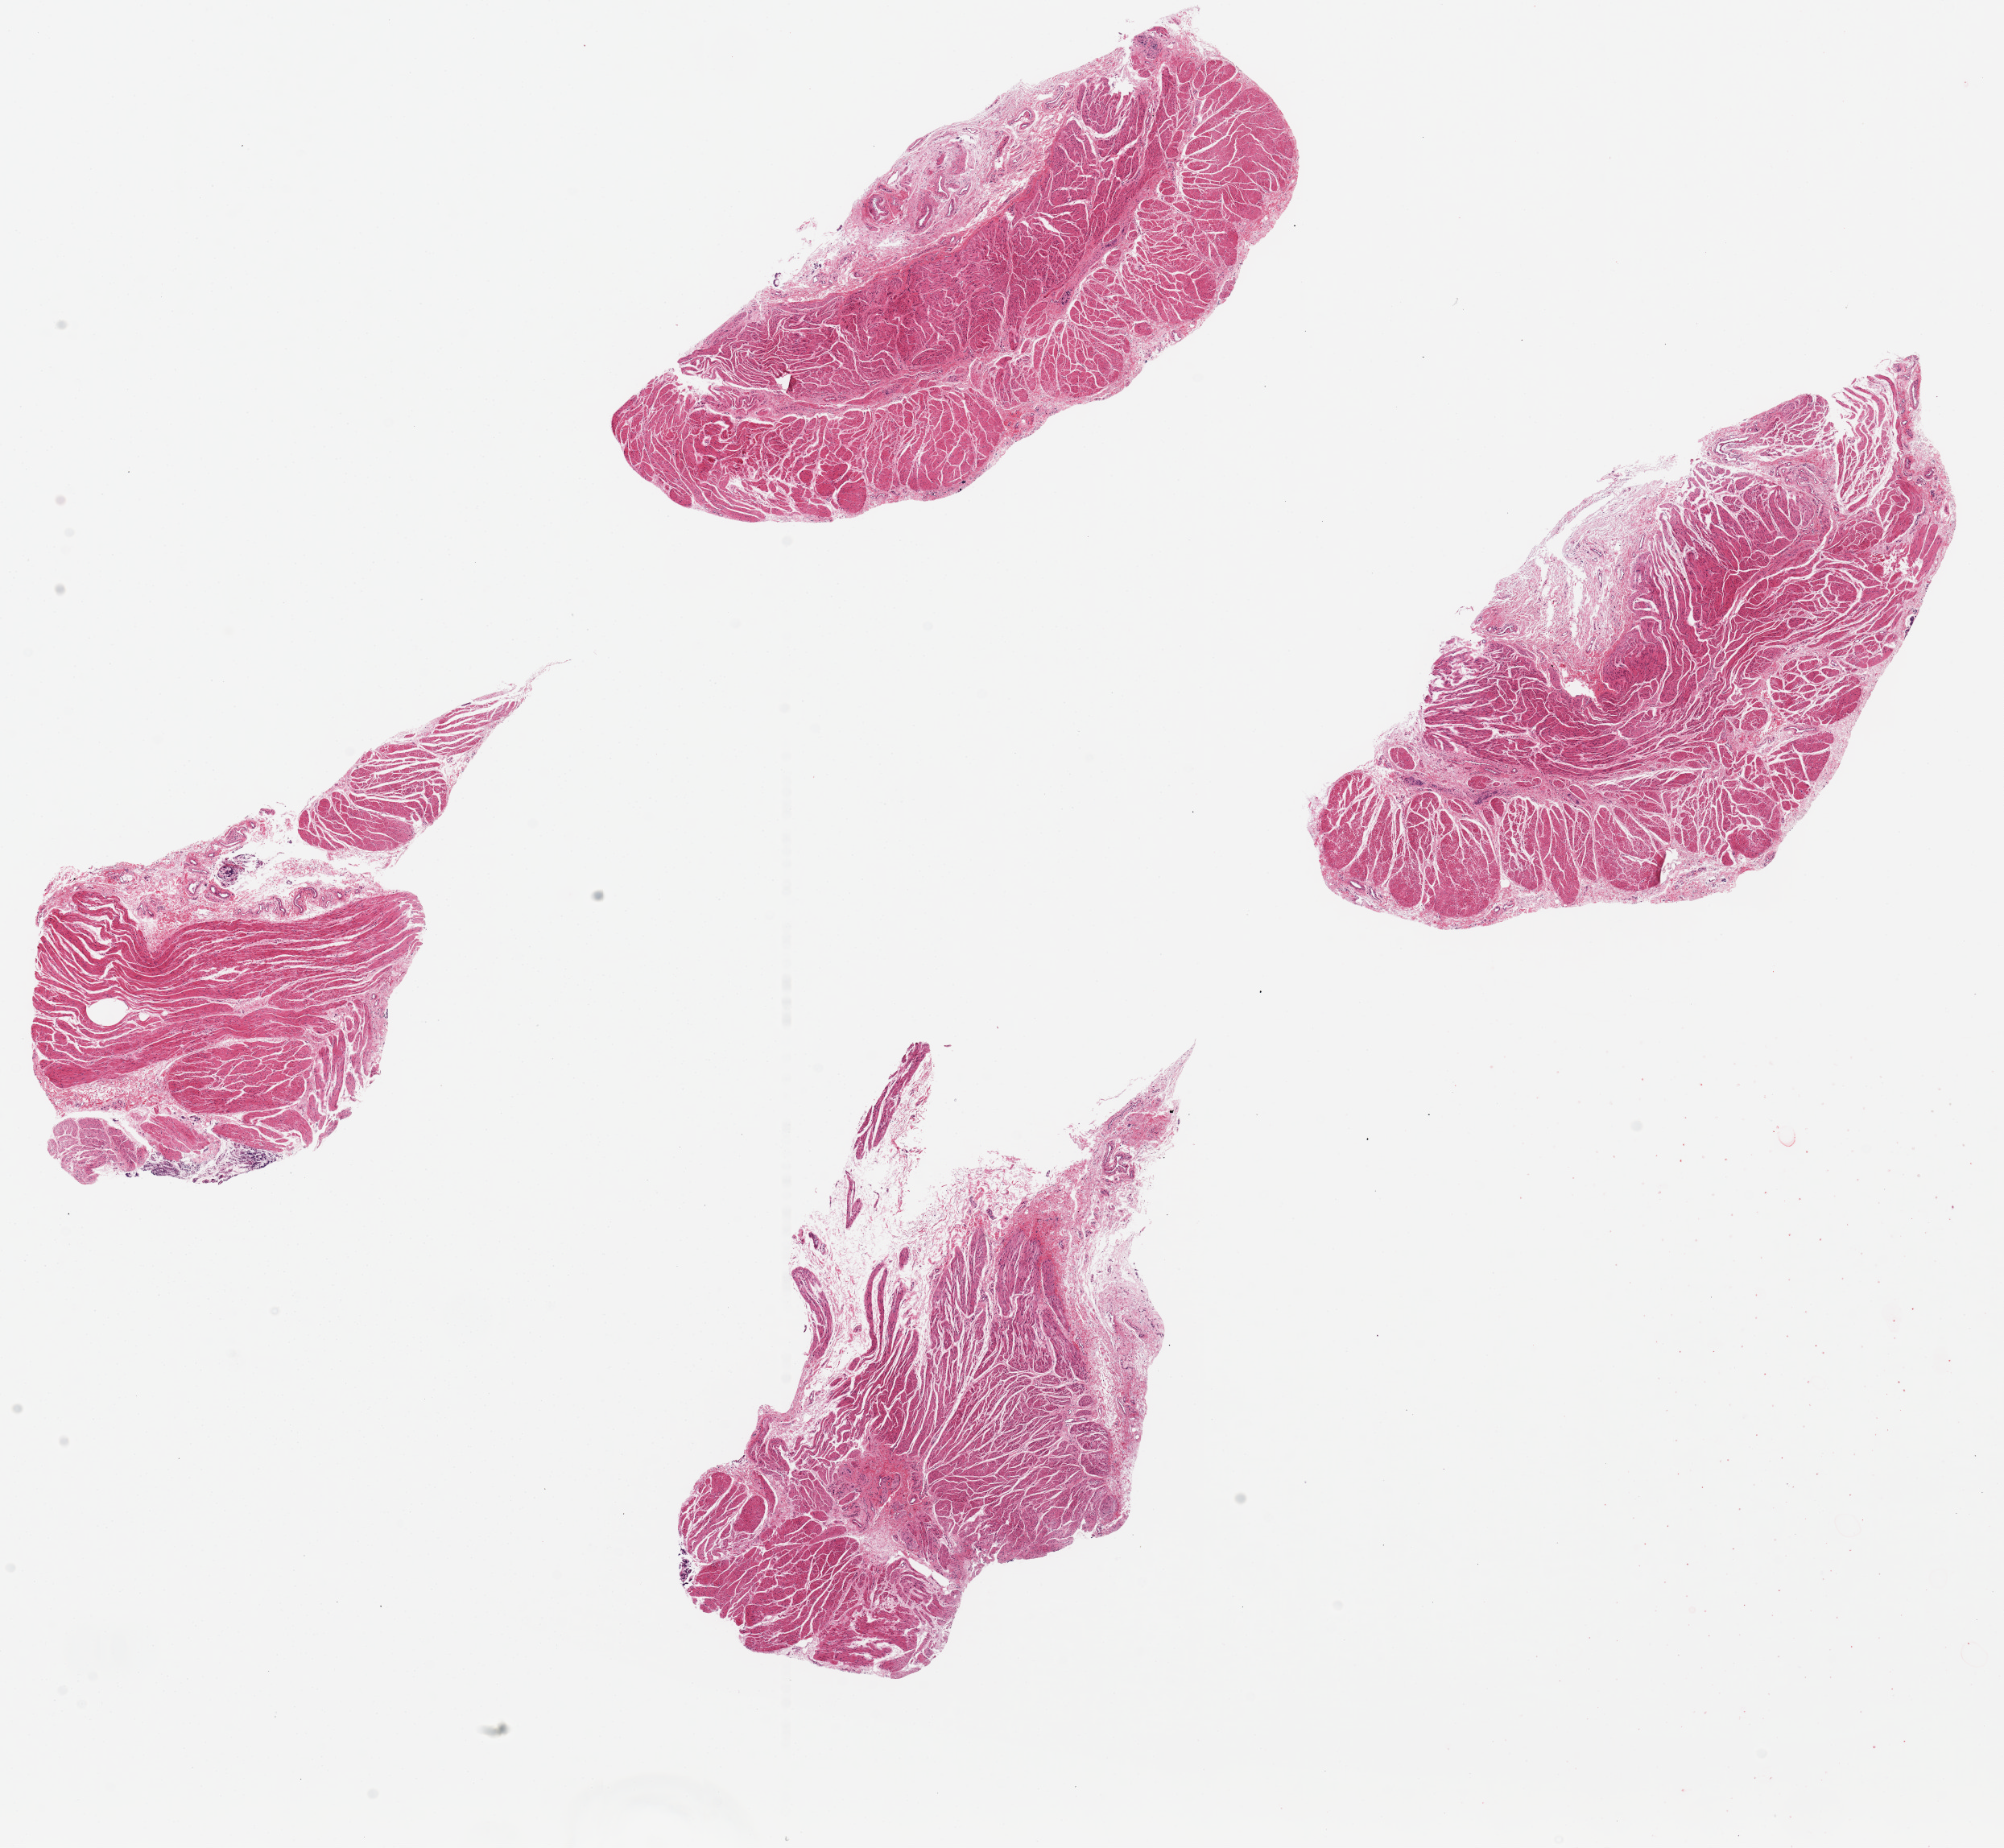
Whole-slide image, haematoxylin and eosin stain — low-resolution overview of the scanned area, about 19.7 x 18.2 mm, PAXgene-fixed paraffin-embedded (PFPE) section, target tissue: gastroesophageal junction, tissue donor sample.
• review note (as recorded): 4 pieces, up to 8x4mm; well trimmed muscle